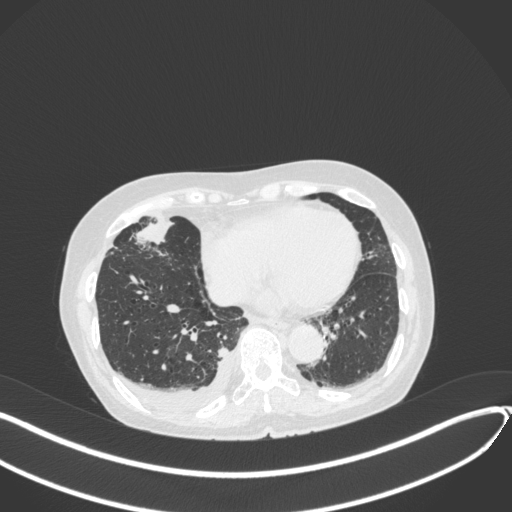
Chest CT, one axial slice. Reconstruction kernel B31f. 120 kVp. Lung window (W 1500 / L -600 HU). 512 × 512 image matrix. Patient: female, 75 years. Case-level facts recorded for this patient, not image findings: clinical TNM (as recorded): T2a N3 M0.
Structures marked on this image (bounding box drawn by a radiologist):
- lung tumour (recorded histology: adenocarcinoma): bounding box [x1, y1, x2, y2] px = [128, 216, 178, 253]